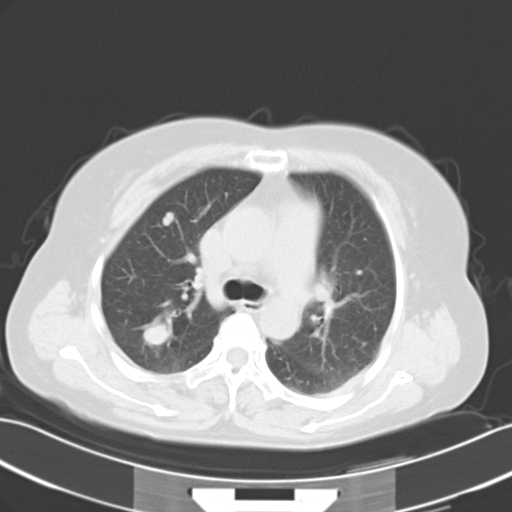
Chest CT, one axial slice. Slice 24 of 35 in the series (ordered by position). Reconstruction kernel B40f. Lung window (W 1500 / L -600 HU). 7 mm slice thickness. 512 × 512 image matrix, field of view 353 × 353 mm. Female patient, age 52 years. Case-level facts recorded for this patient, not image findings: clinical TNM (as recorded): T1c N3 M1a.
Outlined on this slice (bounding box drawn by a radiologist):
- lung tumour (recorded histology: adenocarcinoma): bounding box (x1, y1, x2, y2) in pixels: (131, 309, 187, 353)